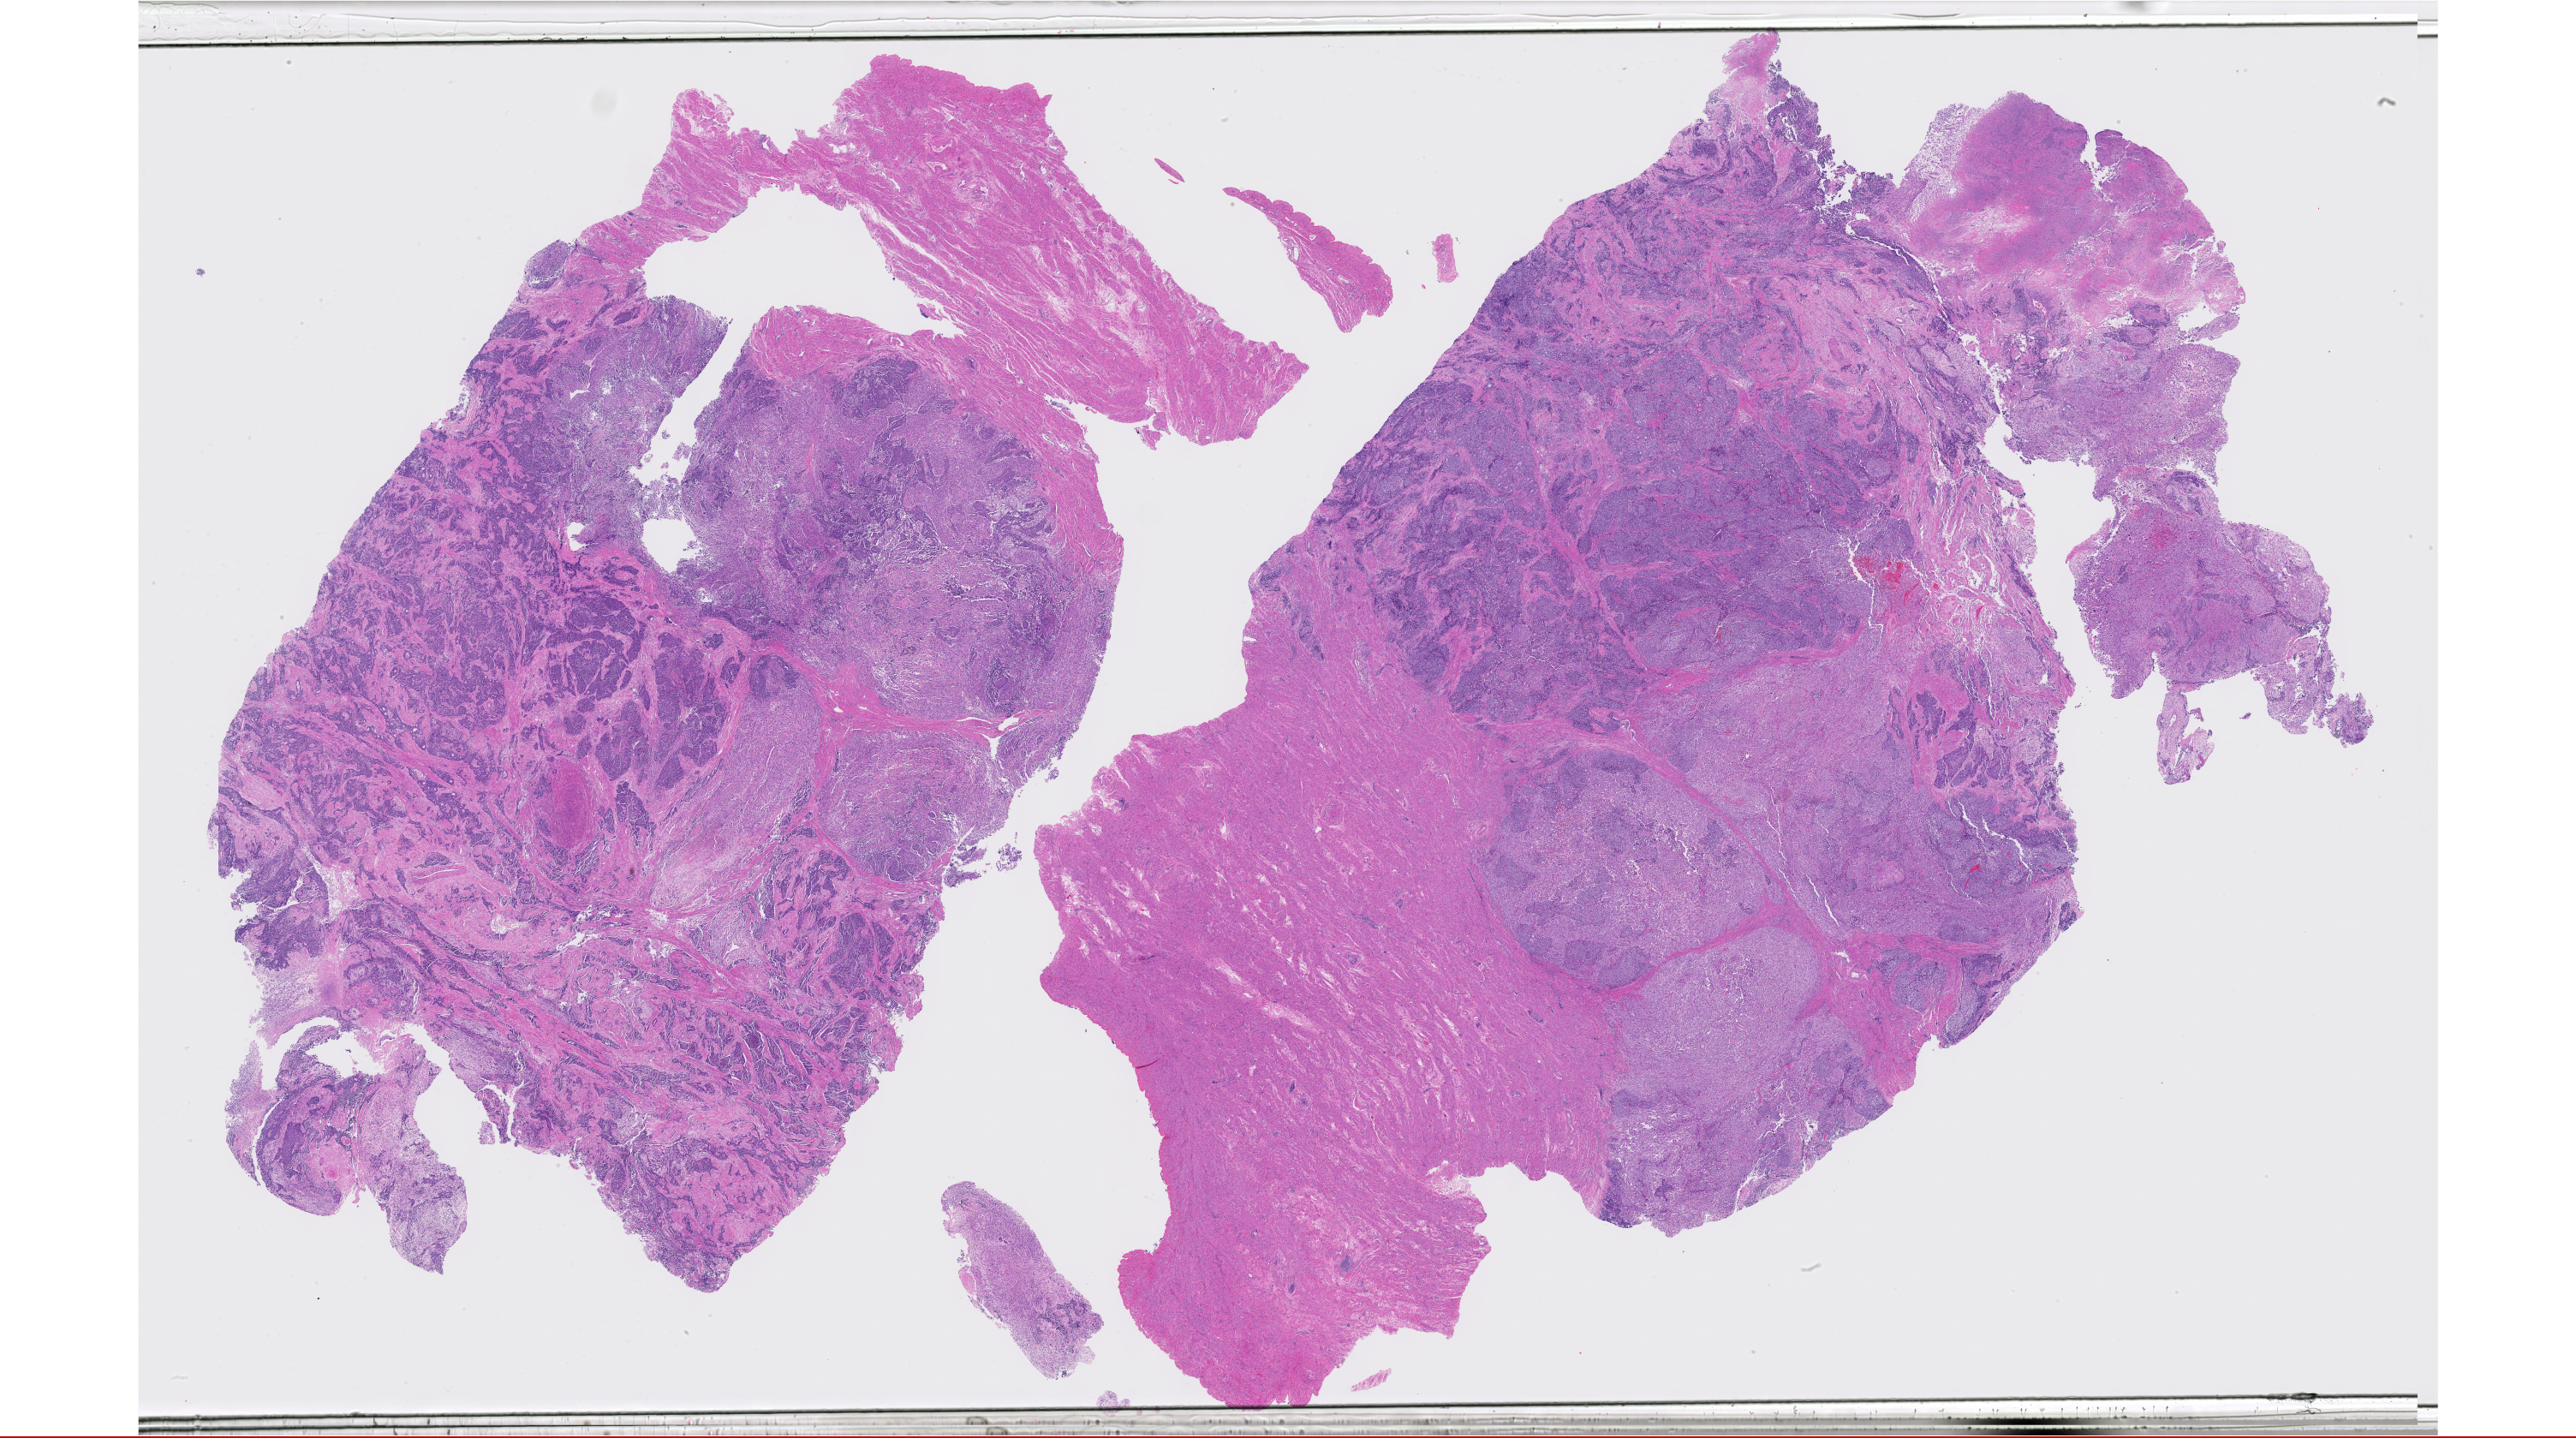
H&E-stained whole-slide image, low-resolution overview of the scanned area, about 48.1 x 26.9 mm; FFPE section; sample: primary tumour, uterus. Female patient; age at initial diagnosis 59 years.
- lymph nodes positive (case pathology): 0 of 16 examined
- pathologic diagnosis: Mullerian mixed tumor
- FIGO stage: II